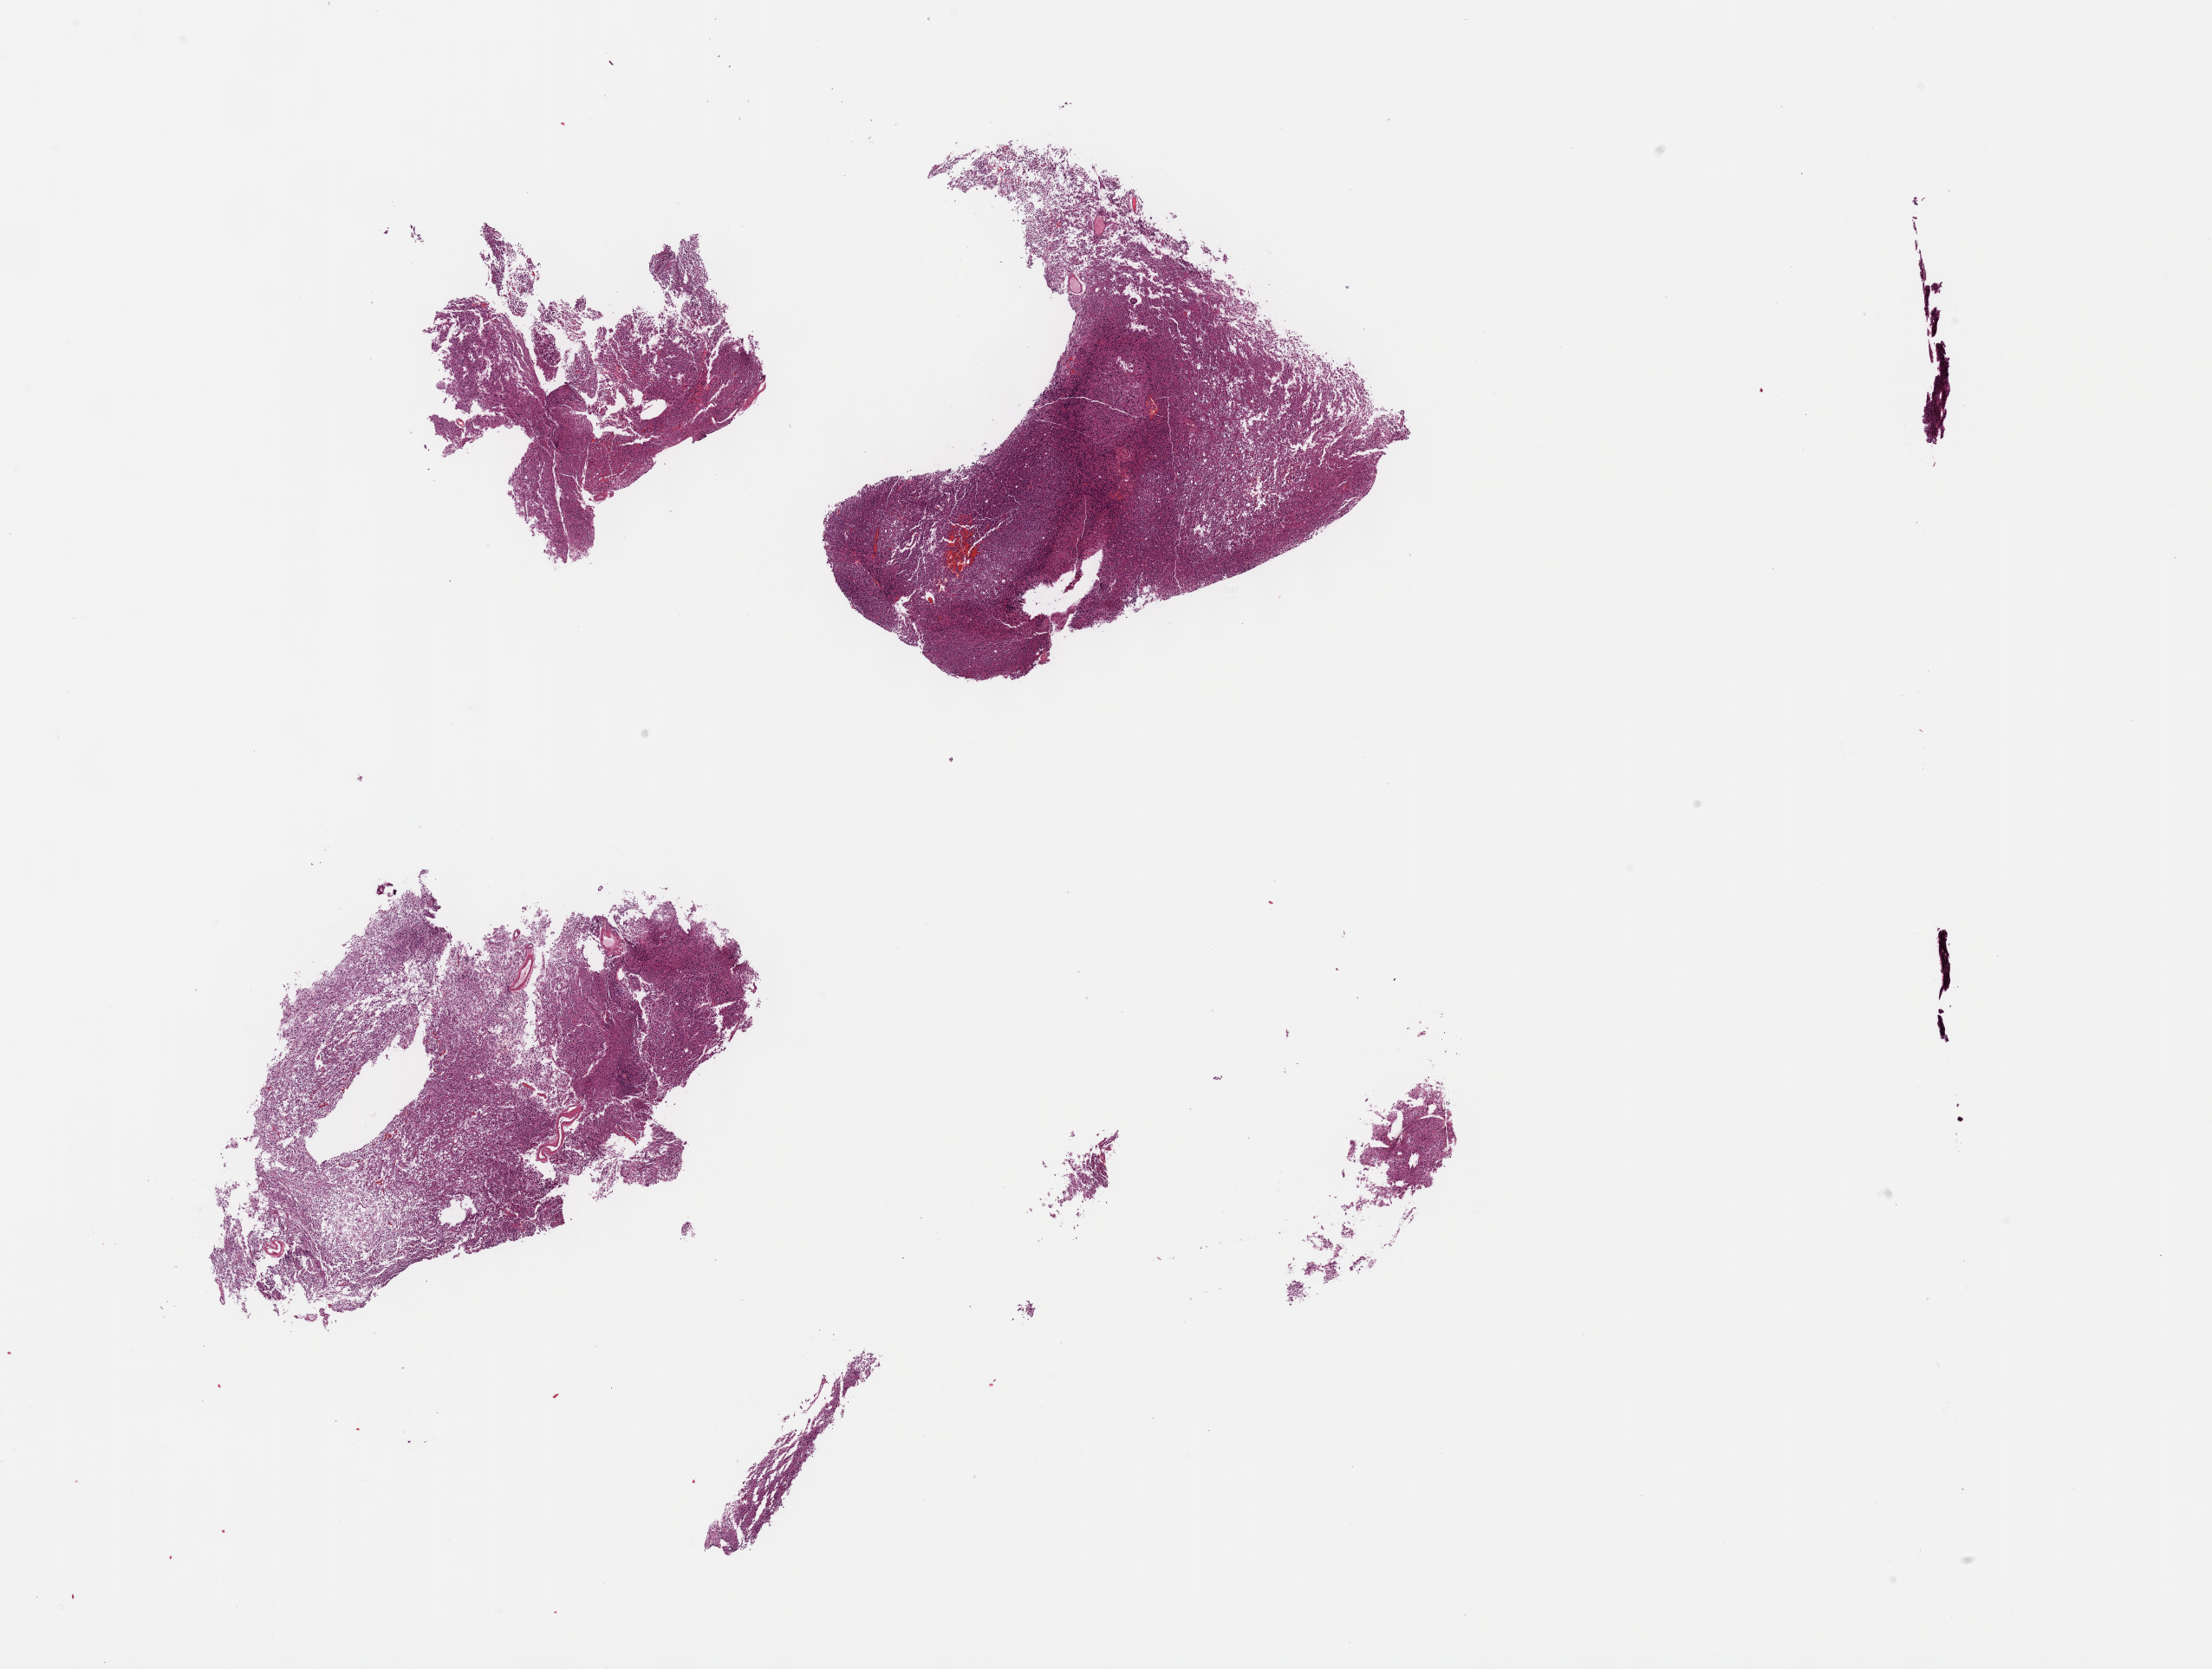
H&E whole-slide image — shown as a low-resolution overview of the whole scanned area (about 20.6 x 15.6 mm, acquisition: 40x scan), formalin-fixed paraffin-embedded (FFPE) diagnostic section, brain, primary tumour sample. Male patient; age at initial diagnosis 53 years. Histologic grade: G3 (poorly differentiated).
Diagnosis: Oligodendroglioma, anaplastic (cerebrum).